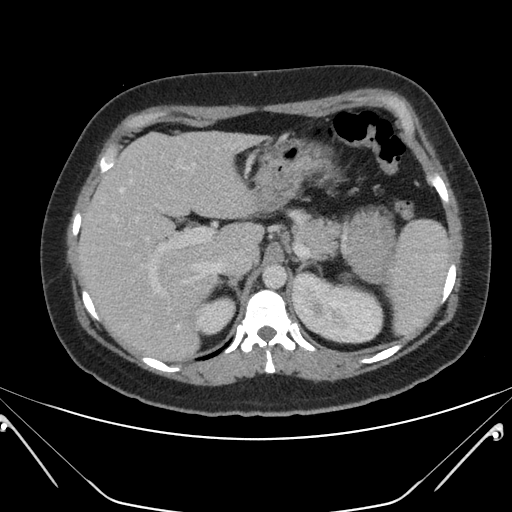
Contrast-enhanced abdominal CT, one axial slice. Slice 132 of 168 in the series (ordered by position). 120 kVp. Intravenous contrast given. Soft-tissue window (W 400 / L 40 HU). 512 × 512 image matrix, field of view 394 × 394 mm. Female patient, age 26 years. From the clinical record (not read from this slice): diagnosis: adrenocortical carcinoma; tumour side: left adrenal; tumour size at pathology: 28 cm.
Outlined on this slice (semi-automatically segmented with operator editing):
- mass: bounding box <348,214,392,282> (left, top, right, bottom; pixels)